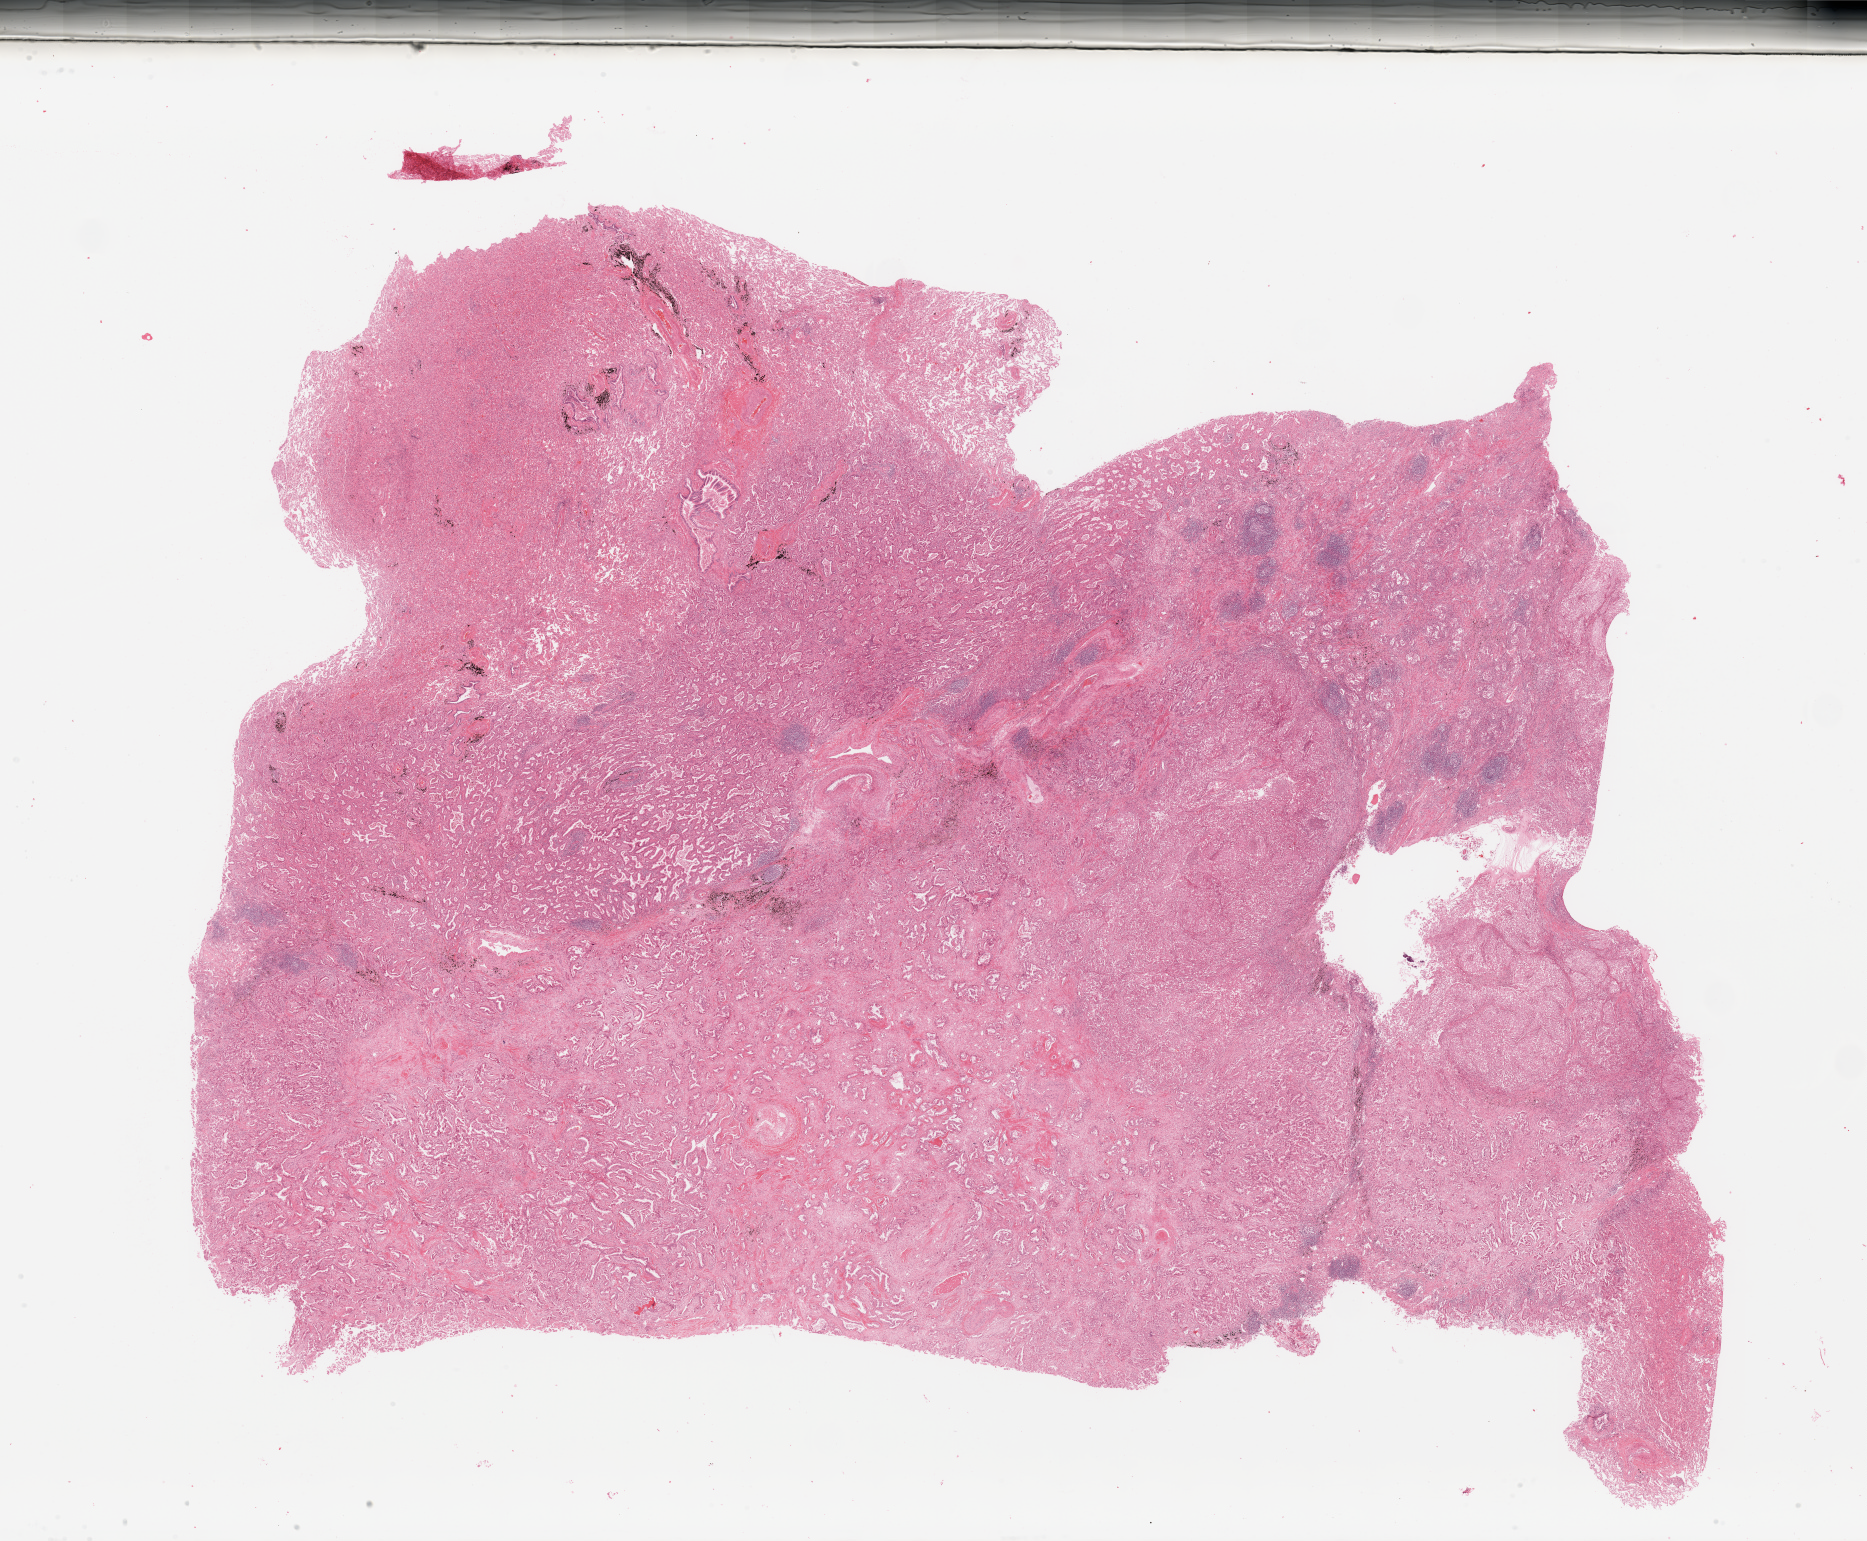
H&E-stained whole-slide image, shown as a low-resolution overview of the whole scanned area (about 29.5 x 24.4 mm). Tumour tissue sample, lung. 47-year-old female patient. Histologic grade: G3 (poorly differentiated).
AJCC pathologic stage: IIIA. Diagnosis: Adenocarcinoma, NOS.